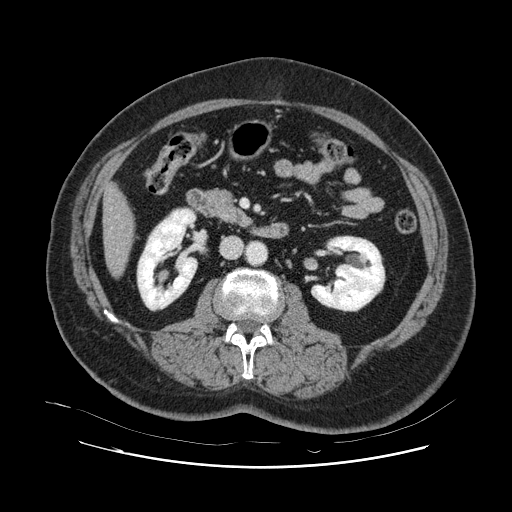
Contrast-enhanced abdominal CT, one axial slice; position 26 of 132 along the scan axis; 120 kVp; intravenous contrast given; soft-tissue window (W 400 / L 40 HU); 2.5 mm slice thickness; 512 × 512 image matrix, field of view 391 × 391 mm. Female patient, age 73 years. From the clinical record (not read from this slice): diagnosis: colorectal cancer liver metastases, imaged before liver resection; multiple liver metastases: no; largest metastasis: 7 cm; chemotherapy before resection: yes.
Structures marked on this image (manually delineated by an expert):
- liver: box from (x=104, y=188) to (x=132, y=275) px
- planned liver remnant (the part of the liver to remain after resection): (x=104, y=188)–(x=133, y=276)